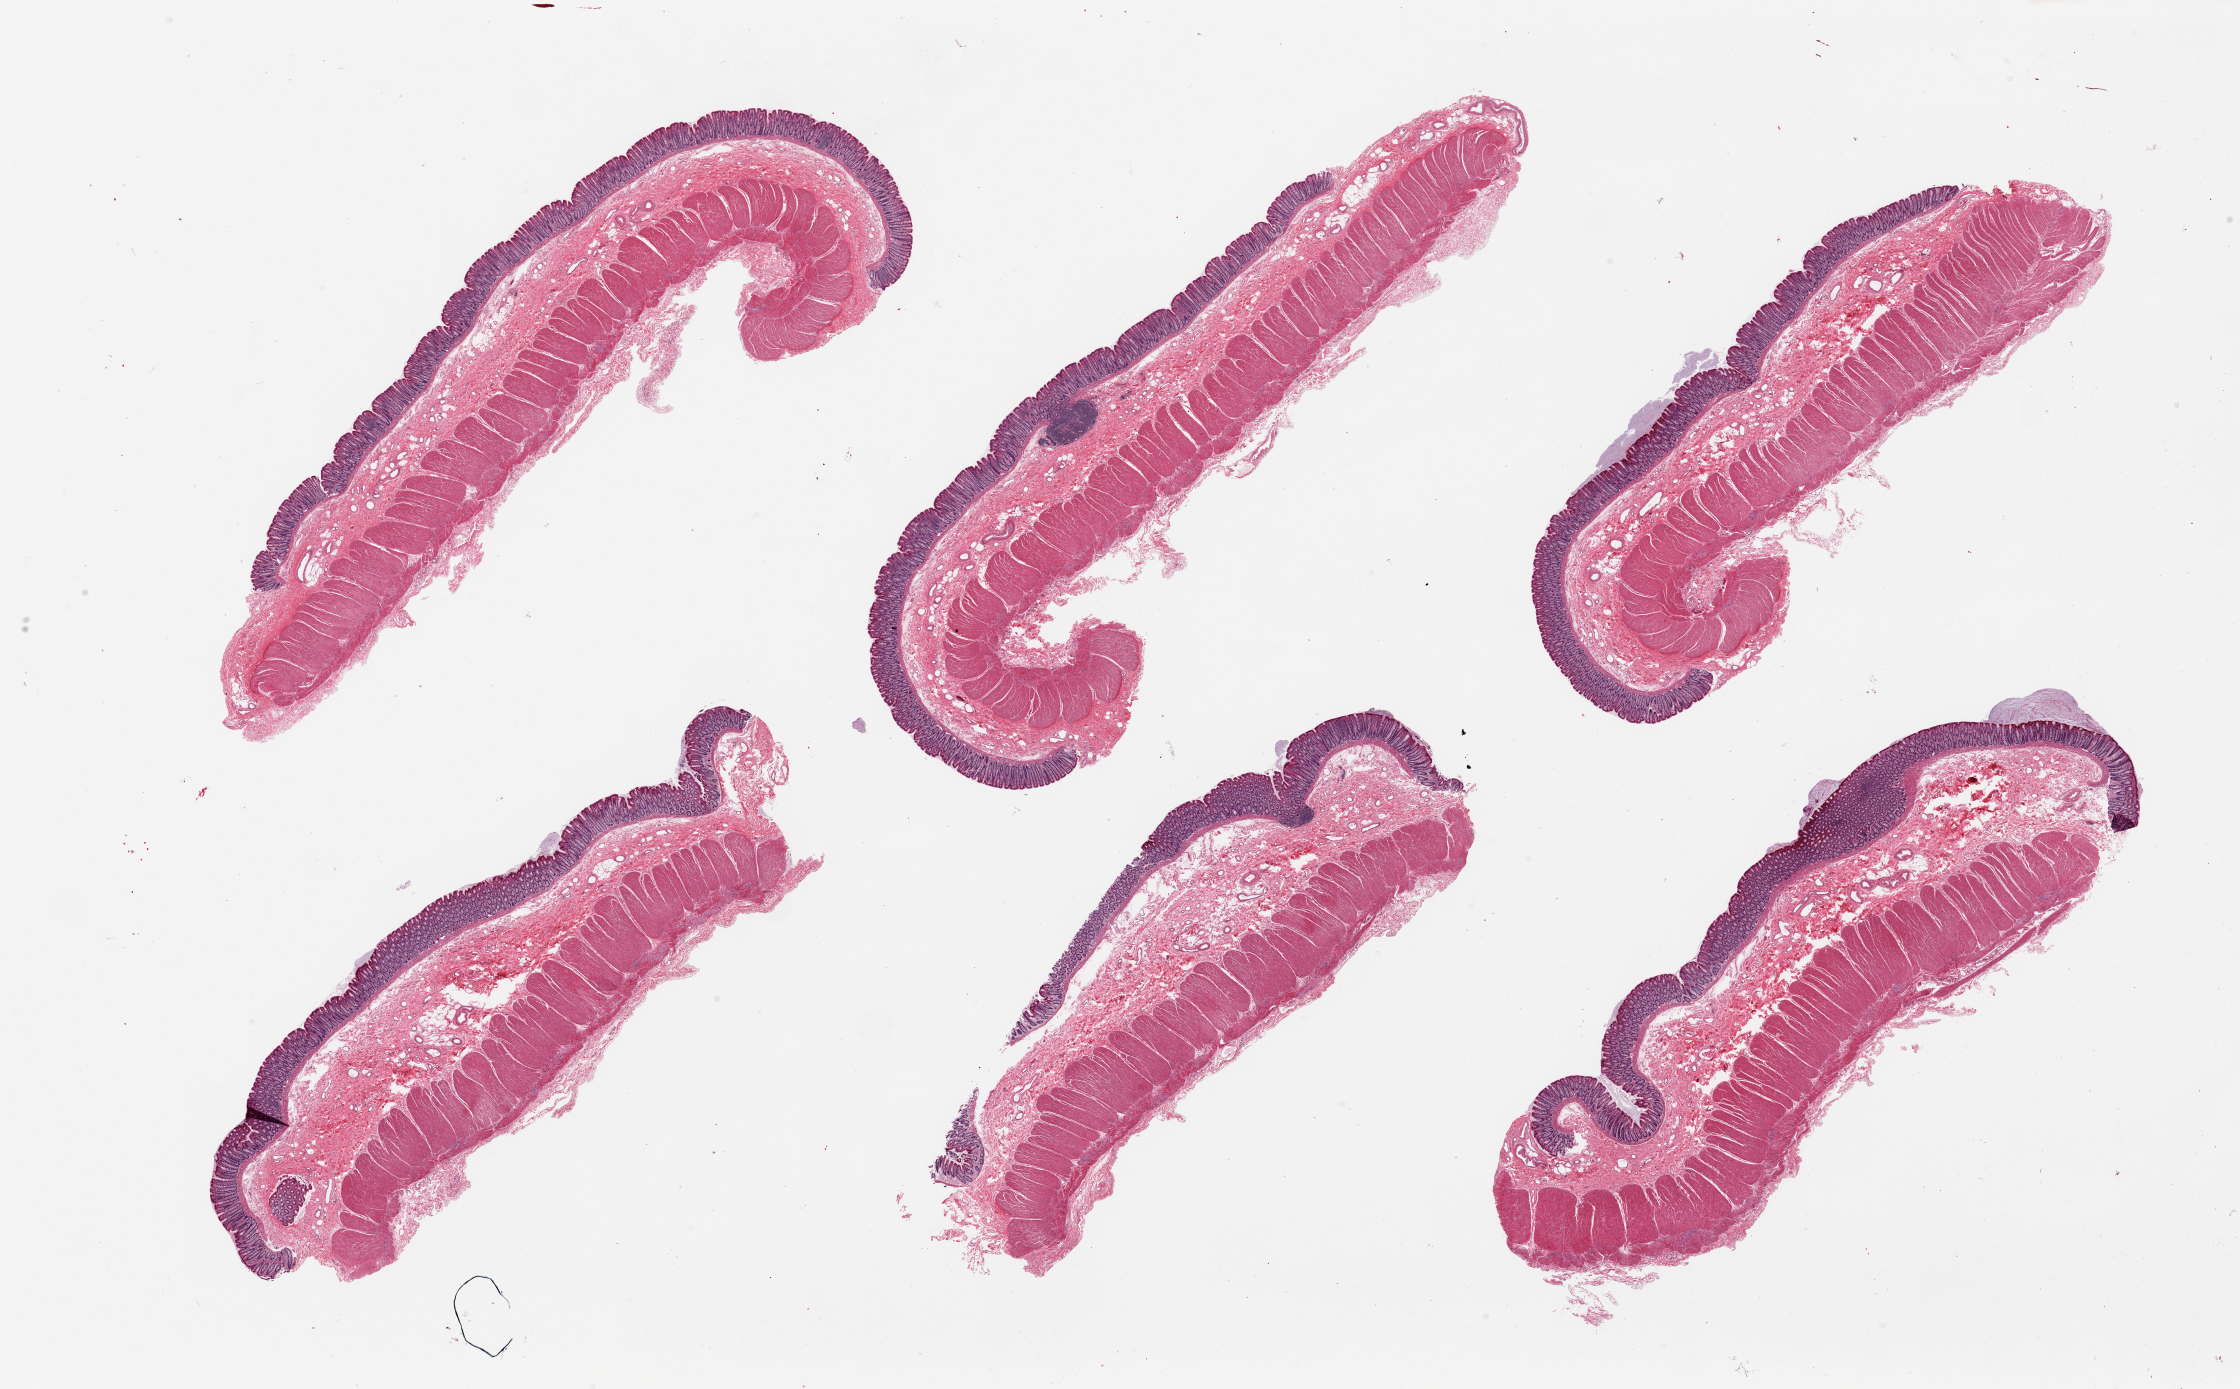
H&E whole-slide image — shown as a low-resolution overview of the whole scanned area (about 35.4 x 22.0 mm). PAXgene-fixed, paraffin-embedded tissue. Sampled site (target tissue): transverse colon. Tissue donor sample. Female donor.
- pathologist's review note for this sample: 6 pieces. Well dissected